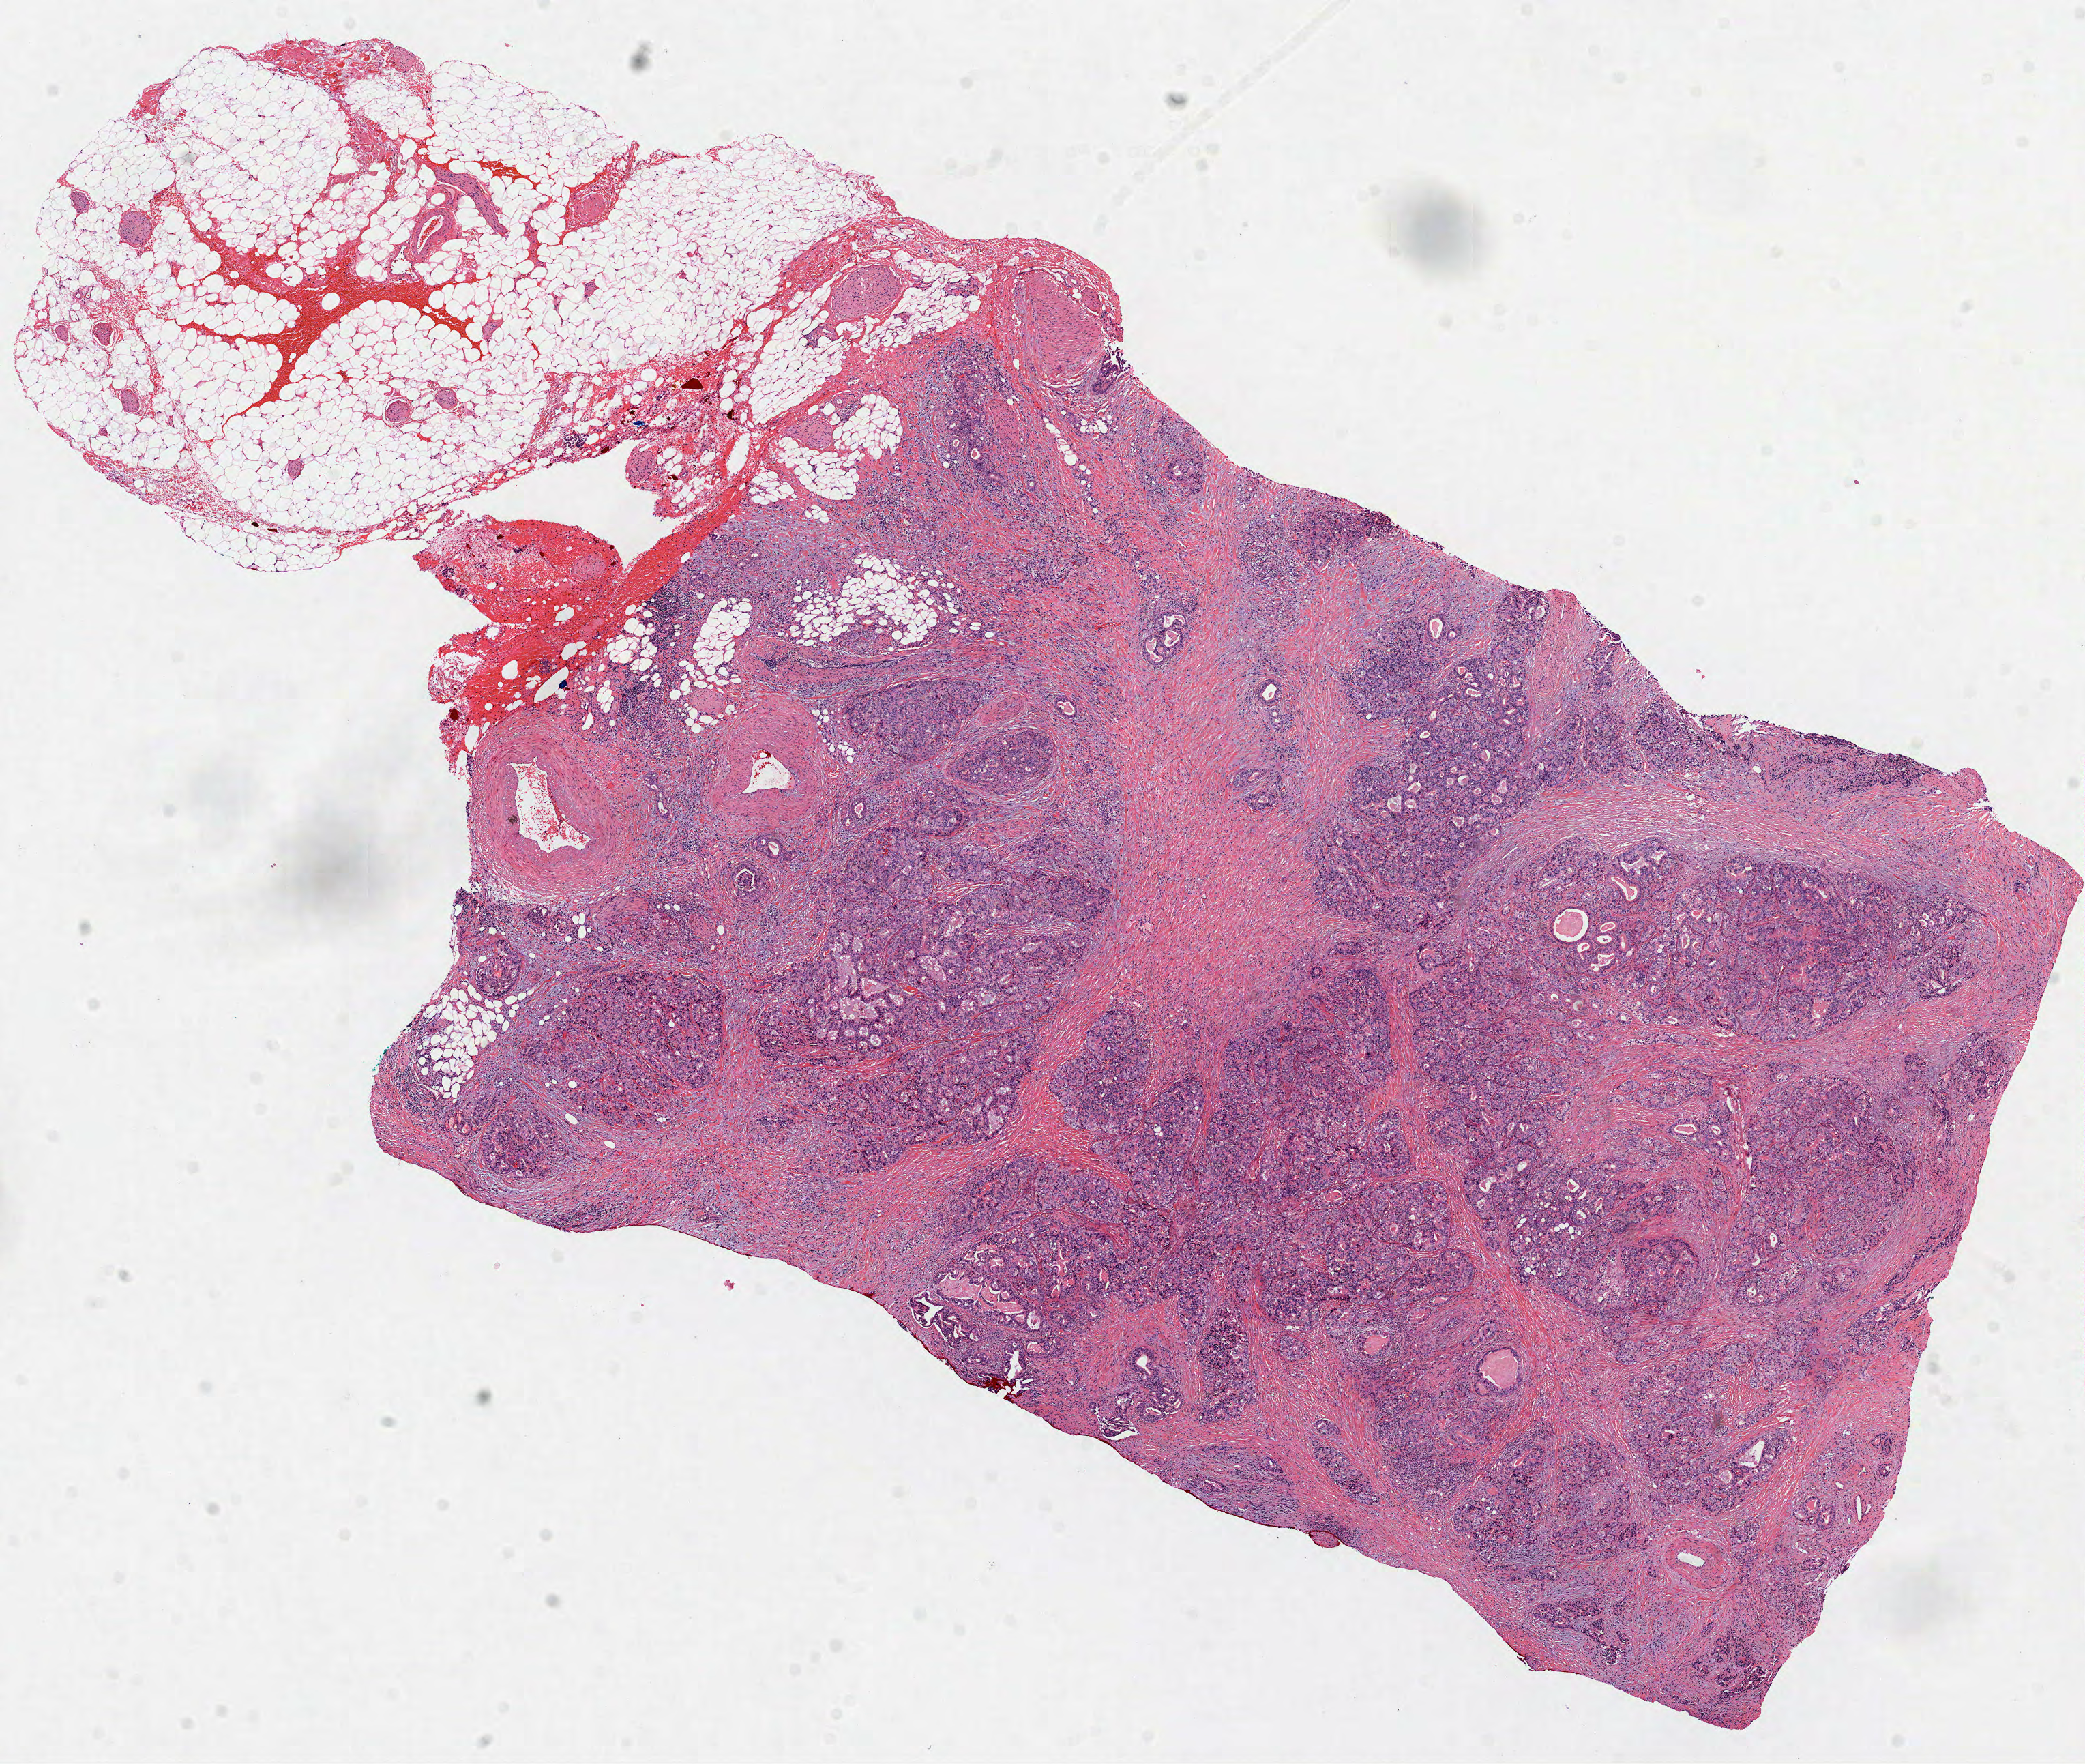
Digitized Hematoxylin and eosin (H&E) stained tissue section (whole slide), low-resolution overview of the scanned area, about 12.3 x 10.4 mm. Formalin-fixed paraffin-embedded (FFPE) diagnostic section. Pancreas, primary tumour sample. Patient: male, age at initial diagnosis 72 years. Histologic grade: G3 (poorly differentiated).
Diagnosis: Infiltrating duct carcinoma, NOS. Lymph nodes positive (case pathology): 11 of 22 examined. AJCC pathologic stage: IIB.